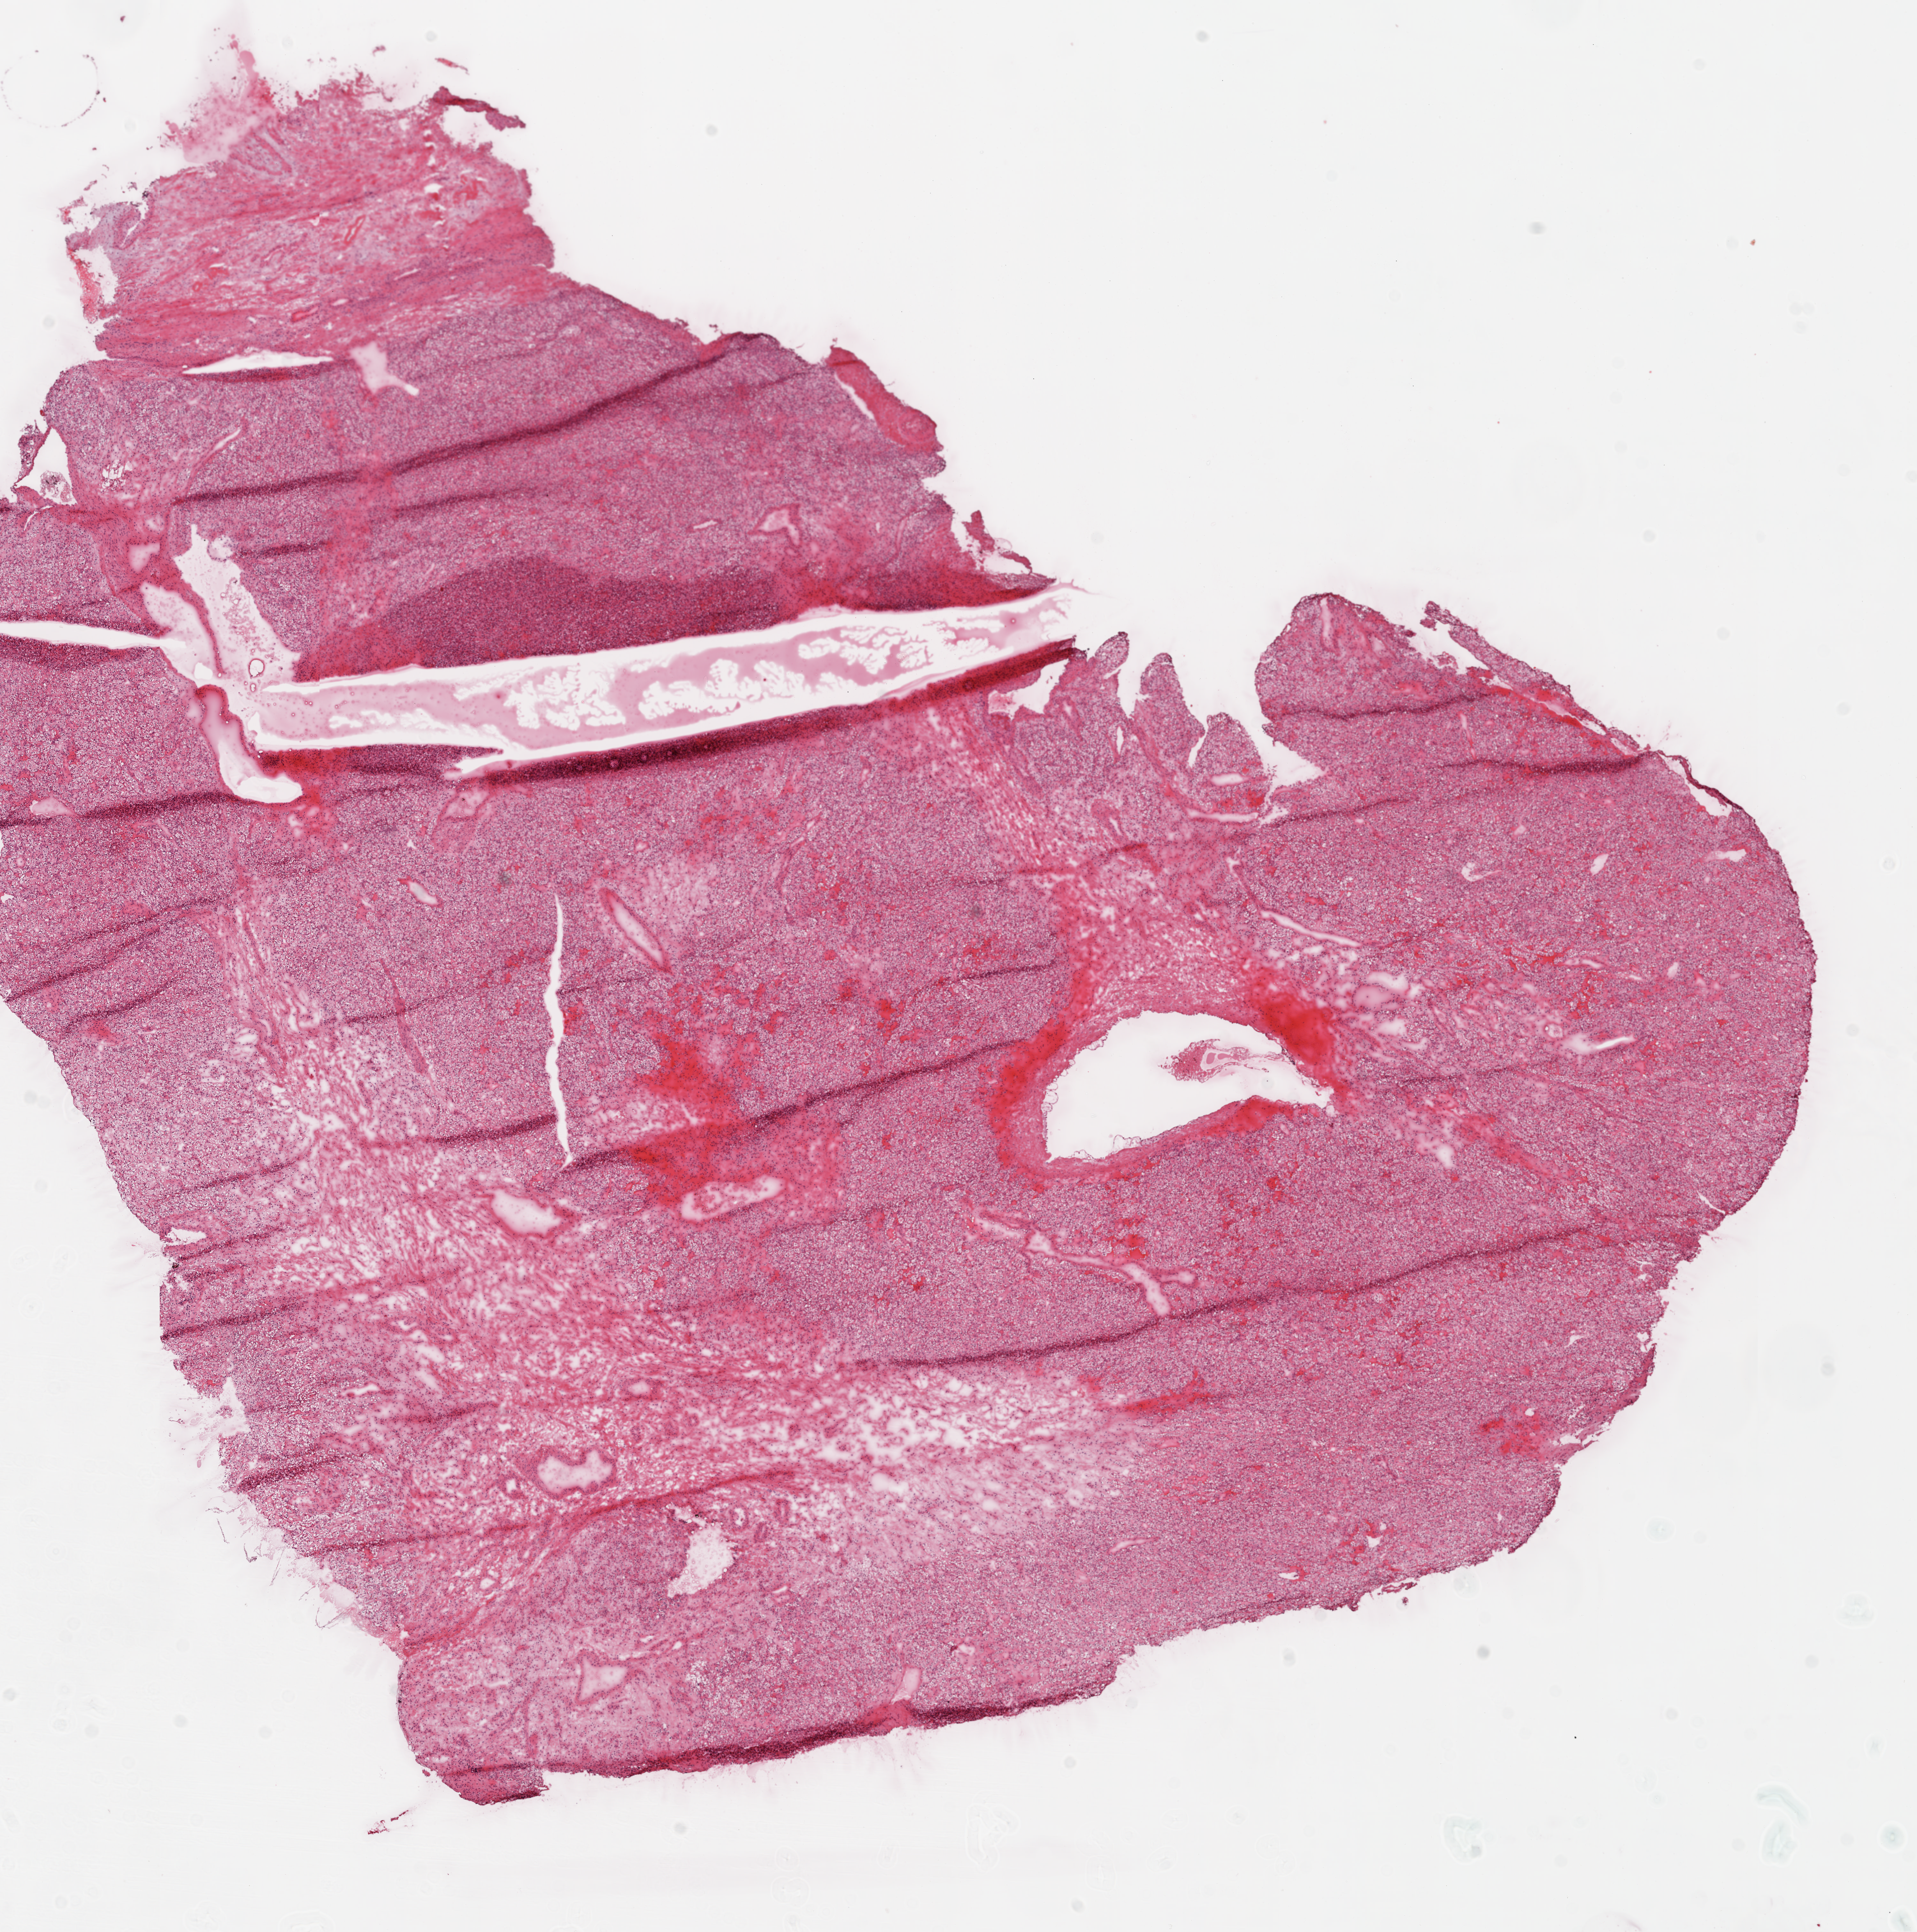
Digitized H&E-stained tissue section (whole slide), a low-resolution overview of the entire scanned area, about 12.0 x 12.1 mm, frozen section from the top of the tissue portion, sample: primary tumour, kidney. Male, age 42 years at initial diagnosis. Histologic grade: G3 (poorly differentiated). Pathologist review of this section (percent, as recorded): tumour cells 75%, tumour nuclei 80%, normal cells 10%, stromal cells 15%, necrosis 0%.
• diagnosis: Clear cell adenocarcinoma, NOS
• AJCC pathologic stage: I